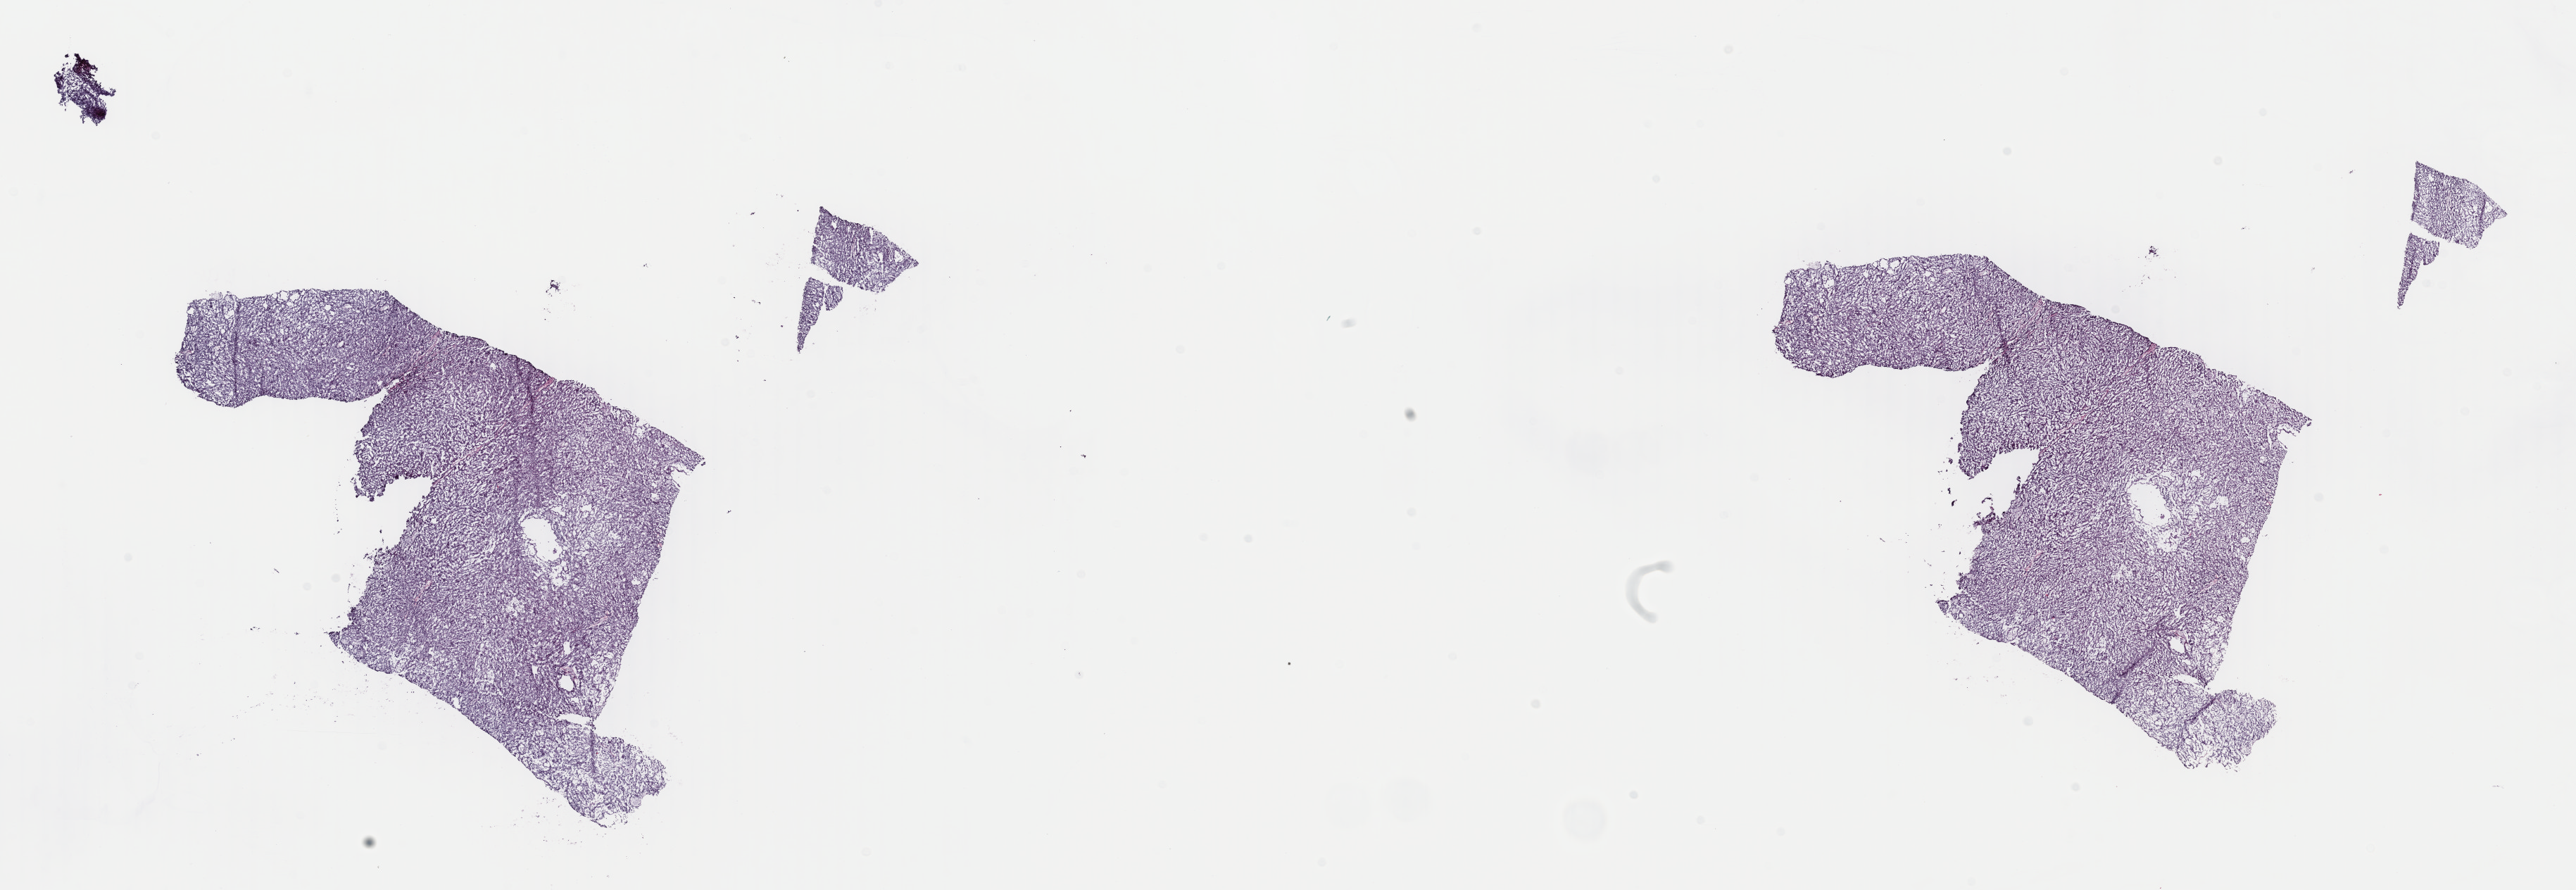
Hematoxylin and eosin (H&E) stained whole-slide image — a low-resolution overview of the entire scanned area, about 28.9 x 10.0 mm (slide scanned at 40x); frozen section; sample: primary tumour, kidney. Patient: male, age at initial diagnosis 57 years. Composition of this section per pathologist review: tumour cells 90%, tumour nuclei 90%, normal cells 0%, stromal cells 10%, necrosis 0%. Infiltration values recorded for this section: lymphocyte infiltration 0%, monocyte infiltration 100%, neutrophil infiltration 0%.
Histologic diagnosis: Papillary adenocarcinoma, NOS. AJCC pathologic stage: I.